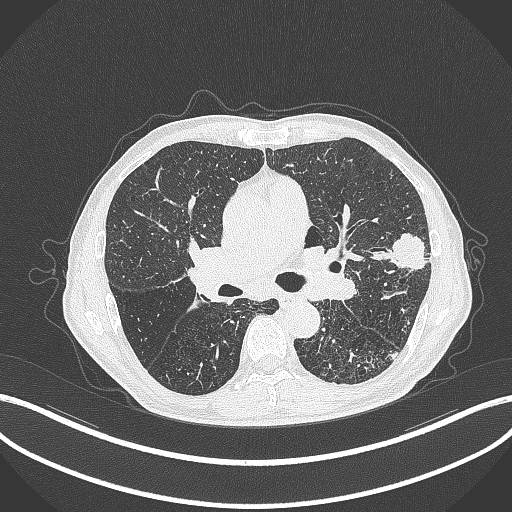
Chest CT, one axial slice; position 244 of 463 along the scan axis; lung window (W 1500 / L -600 HU); 1 mm slice thickness; 512 × 512 image matrix, field of view 400 × 400 mm. Patient: male, 74 years. From the clinical record (not read from this slice): clinical TNM (as recorded): T2a N1 M0.
Outlined on this slice (rectangle marked by the reading radiologist):
- lung tumour (recorded histology: adenocarcinoma): box from (x=370, y=233) to (x=427, y=277) px